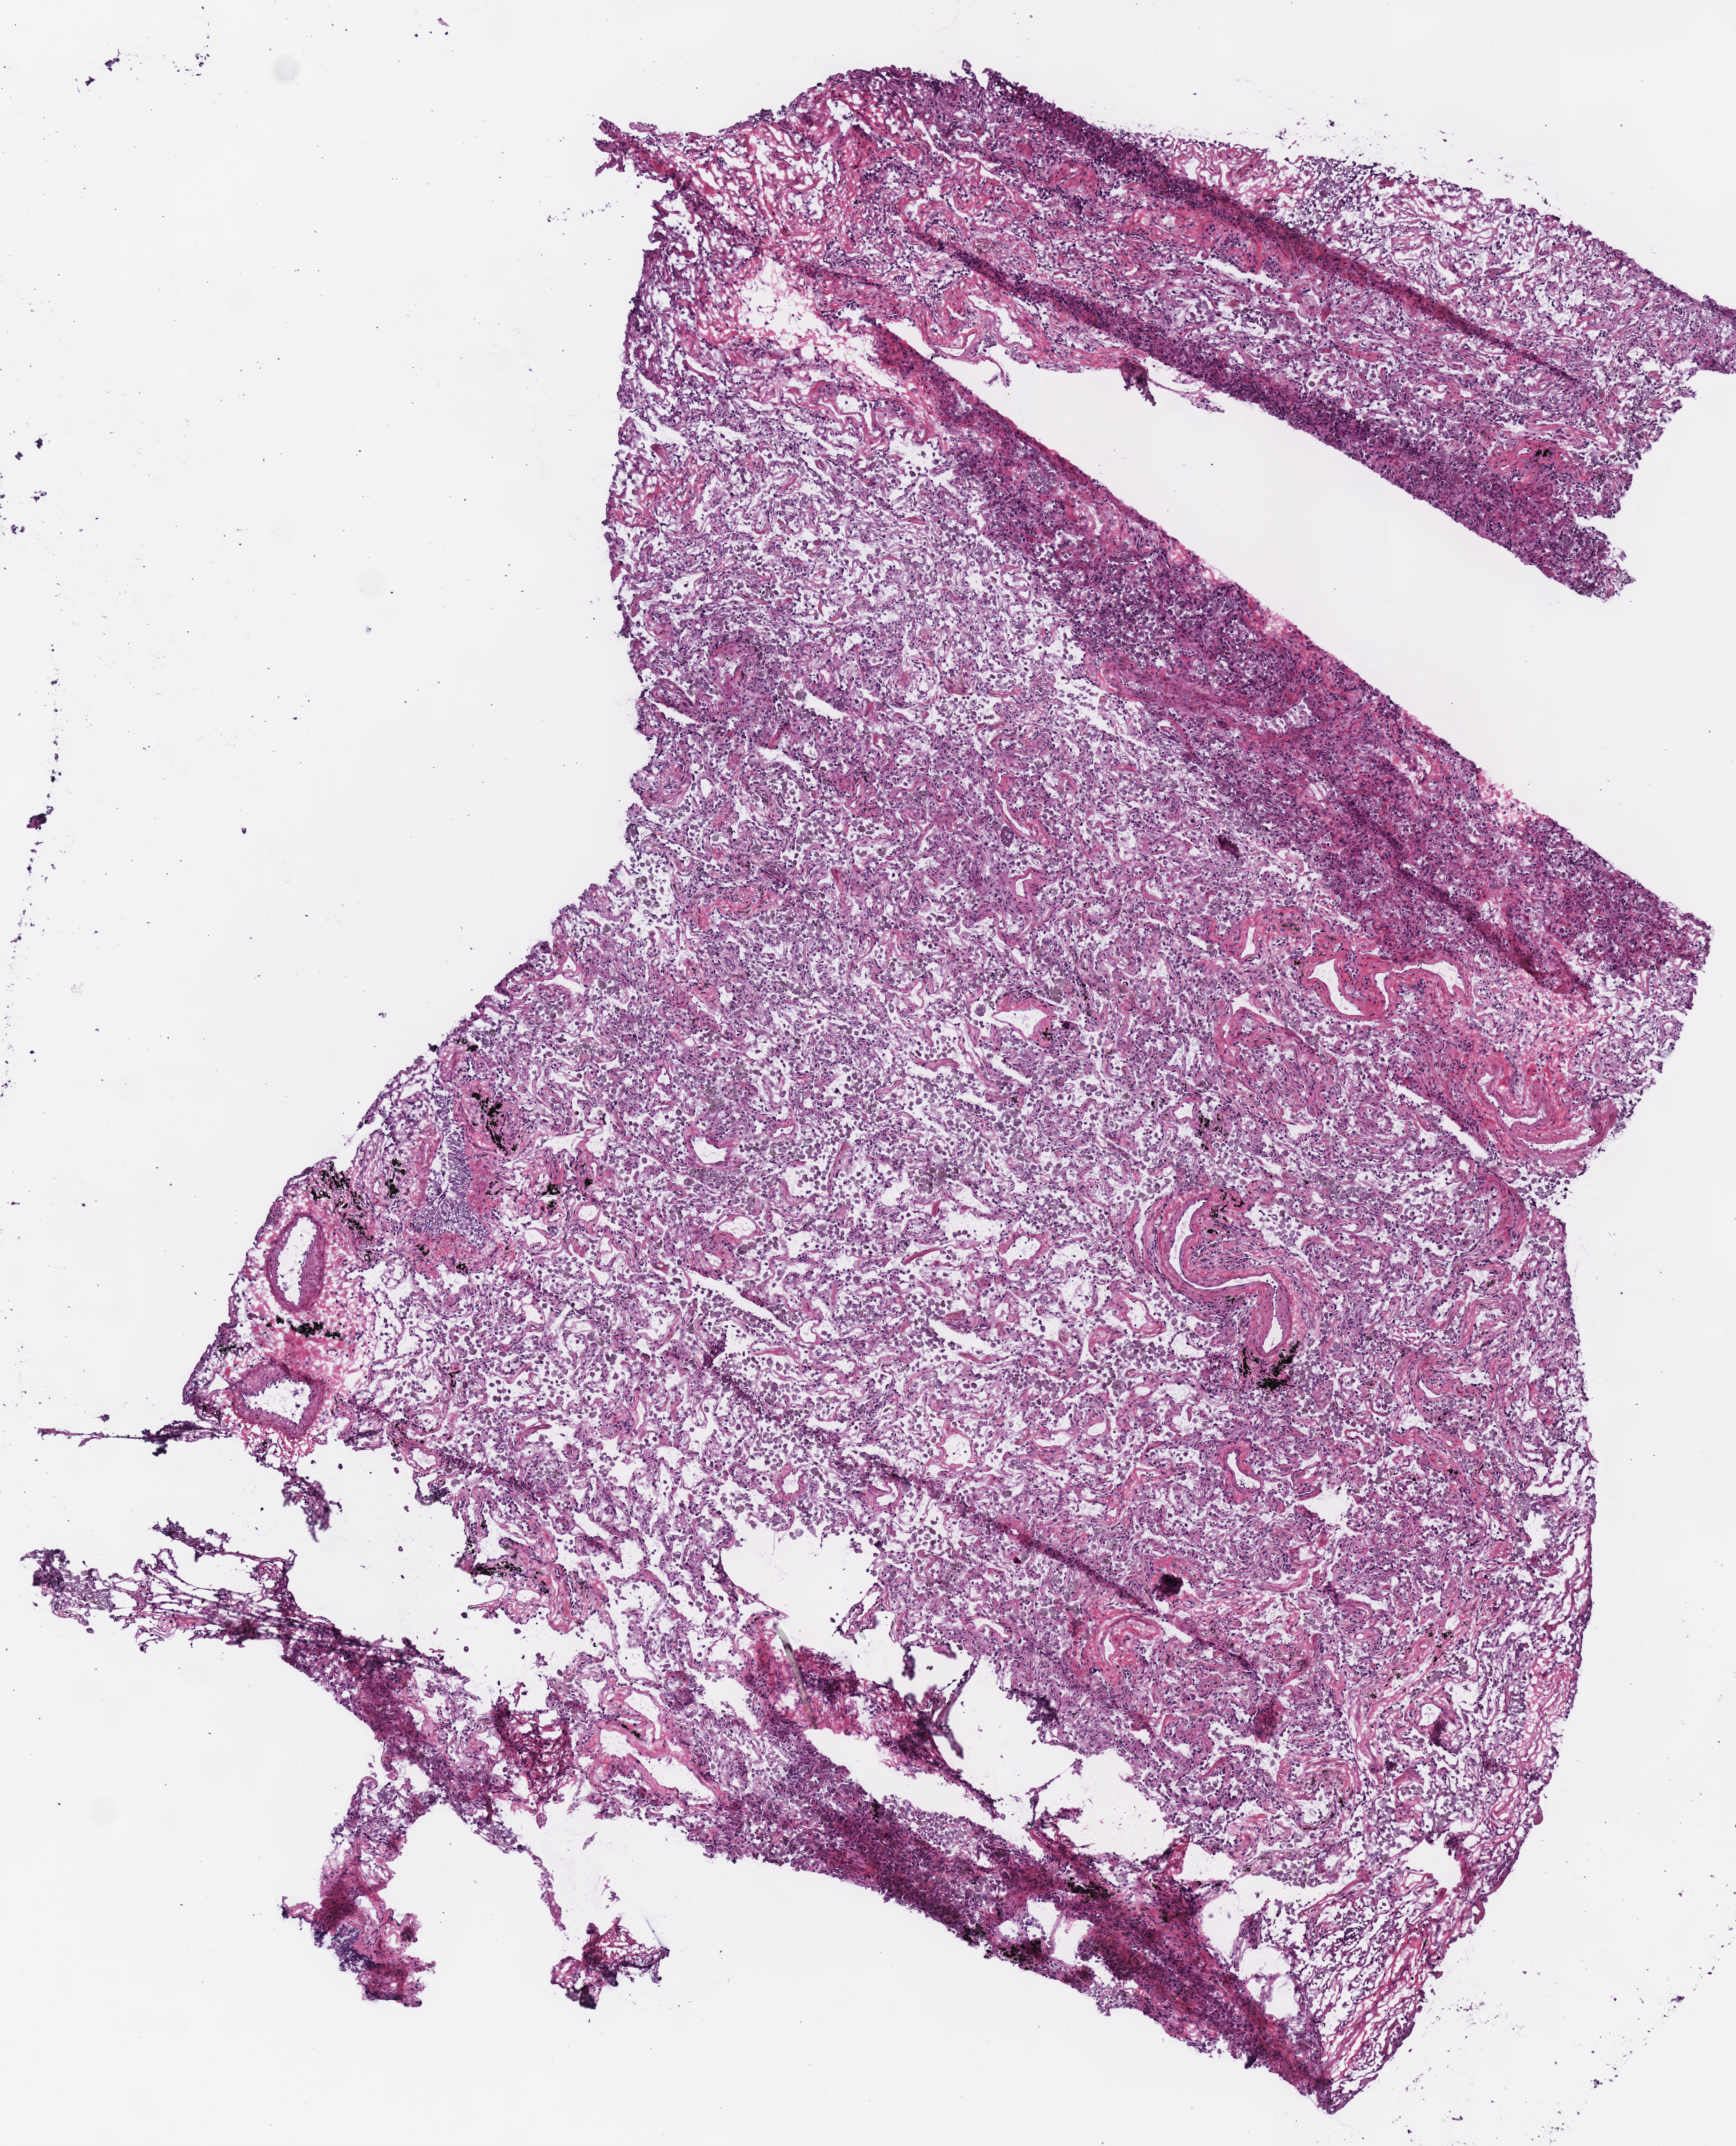
Digitized H&E tissue section (whole slide), low-resolution overview of the scanned area, about 4.9 x 6.0 mm, frozen section from the top of the tissue portion, solid tissue normal (non-tumour tissue) sample from the lung. Patient: female, age at initial diagnosis 57 years.
This section: solid tissue normal (non-tumour) sample from the same patient. Patient diagnosis: Squamous cell carcinoma, NOS.